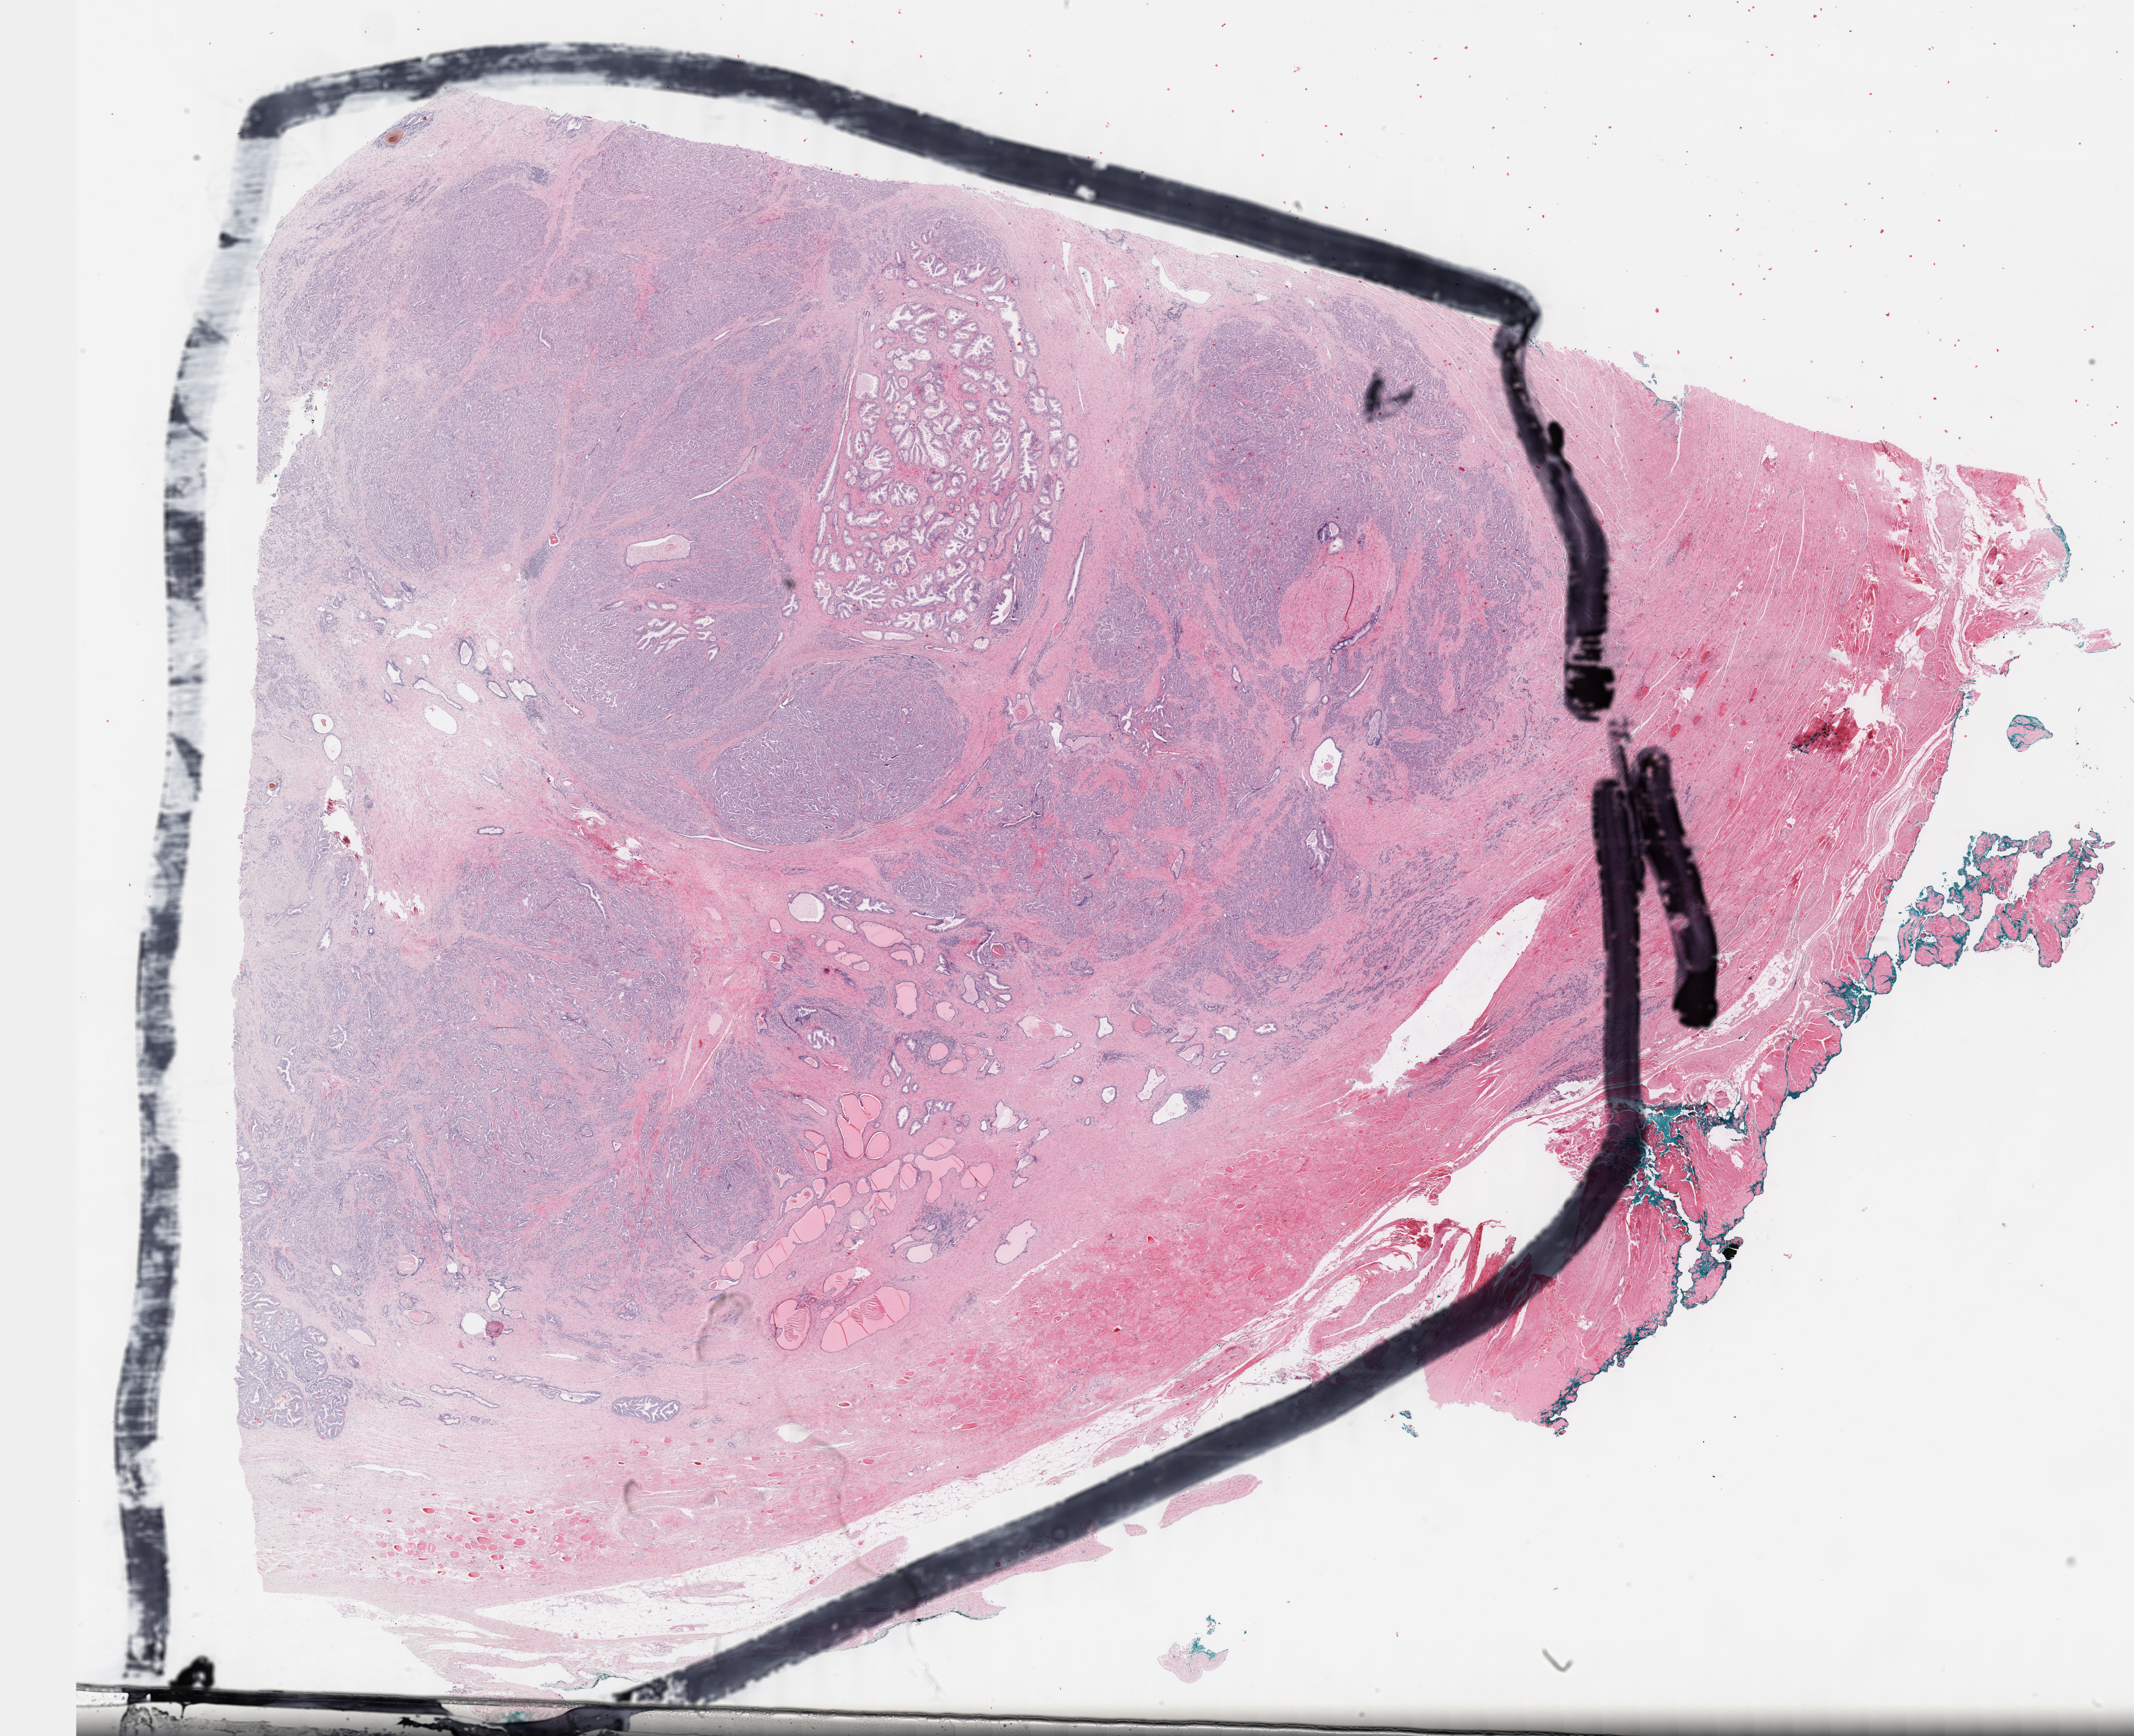
Whole-slide histology image, H&E-stained — a low-resolution overview of the entire scanned area, about 27.7 x 22.6 mm (acquisition: 40x scan), formalin-fixed paraffin-embedded (FFPE) diagnostic section, prostate, primary tumour sample. Male patient; age at initial diagnosis 58 years. Gleason score: 9 (4+5).
* laterality: bilateral
* histologic diagnosis: Adenocarcinoma, NOS (prostate gland)
* lymph nodes positive (case pathology): 2 of 8 examined